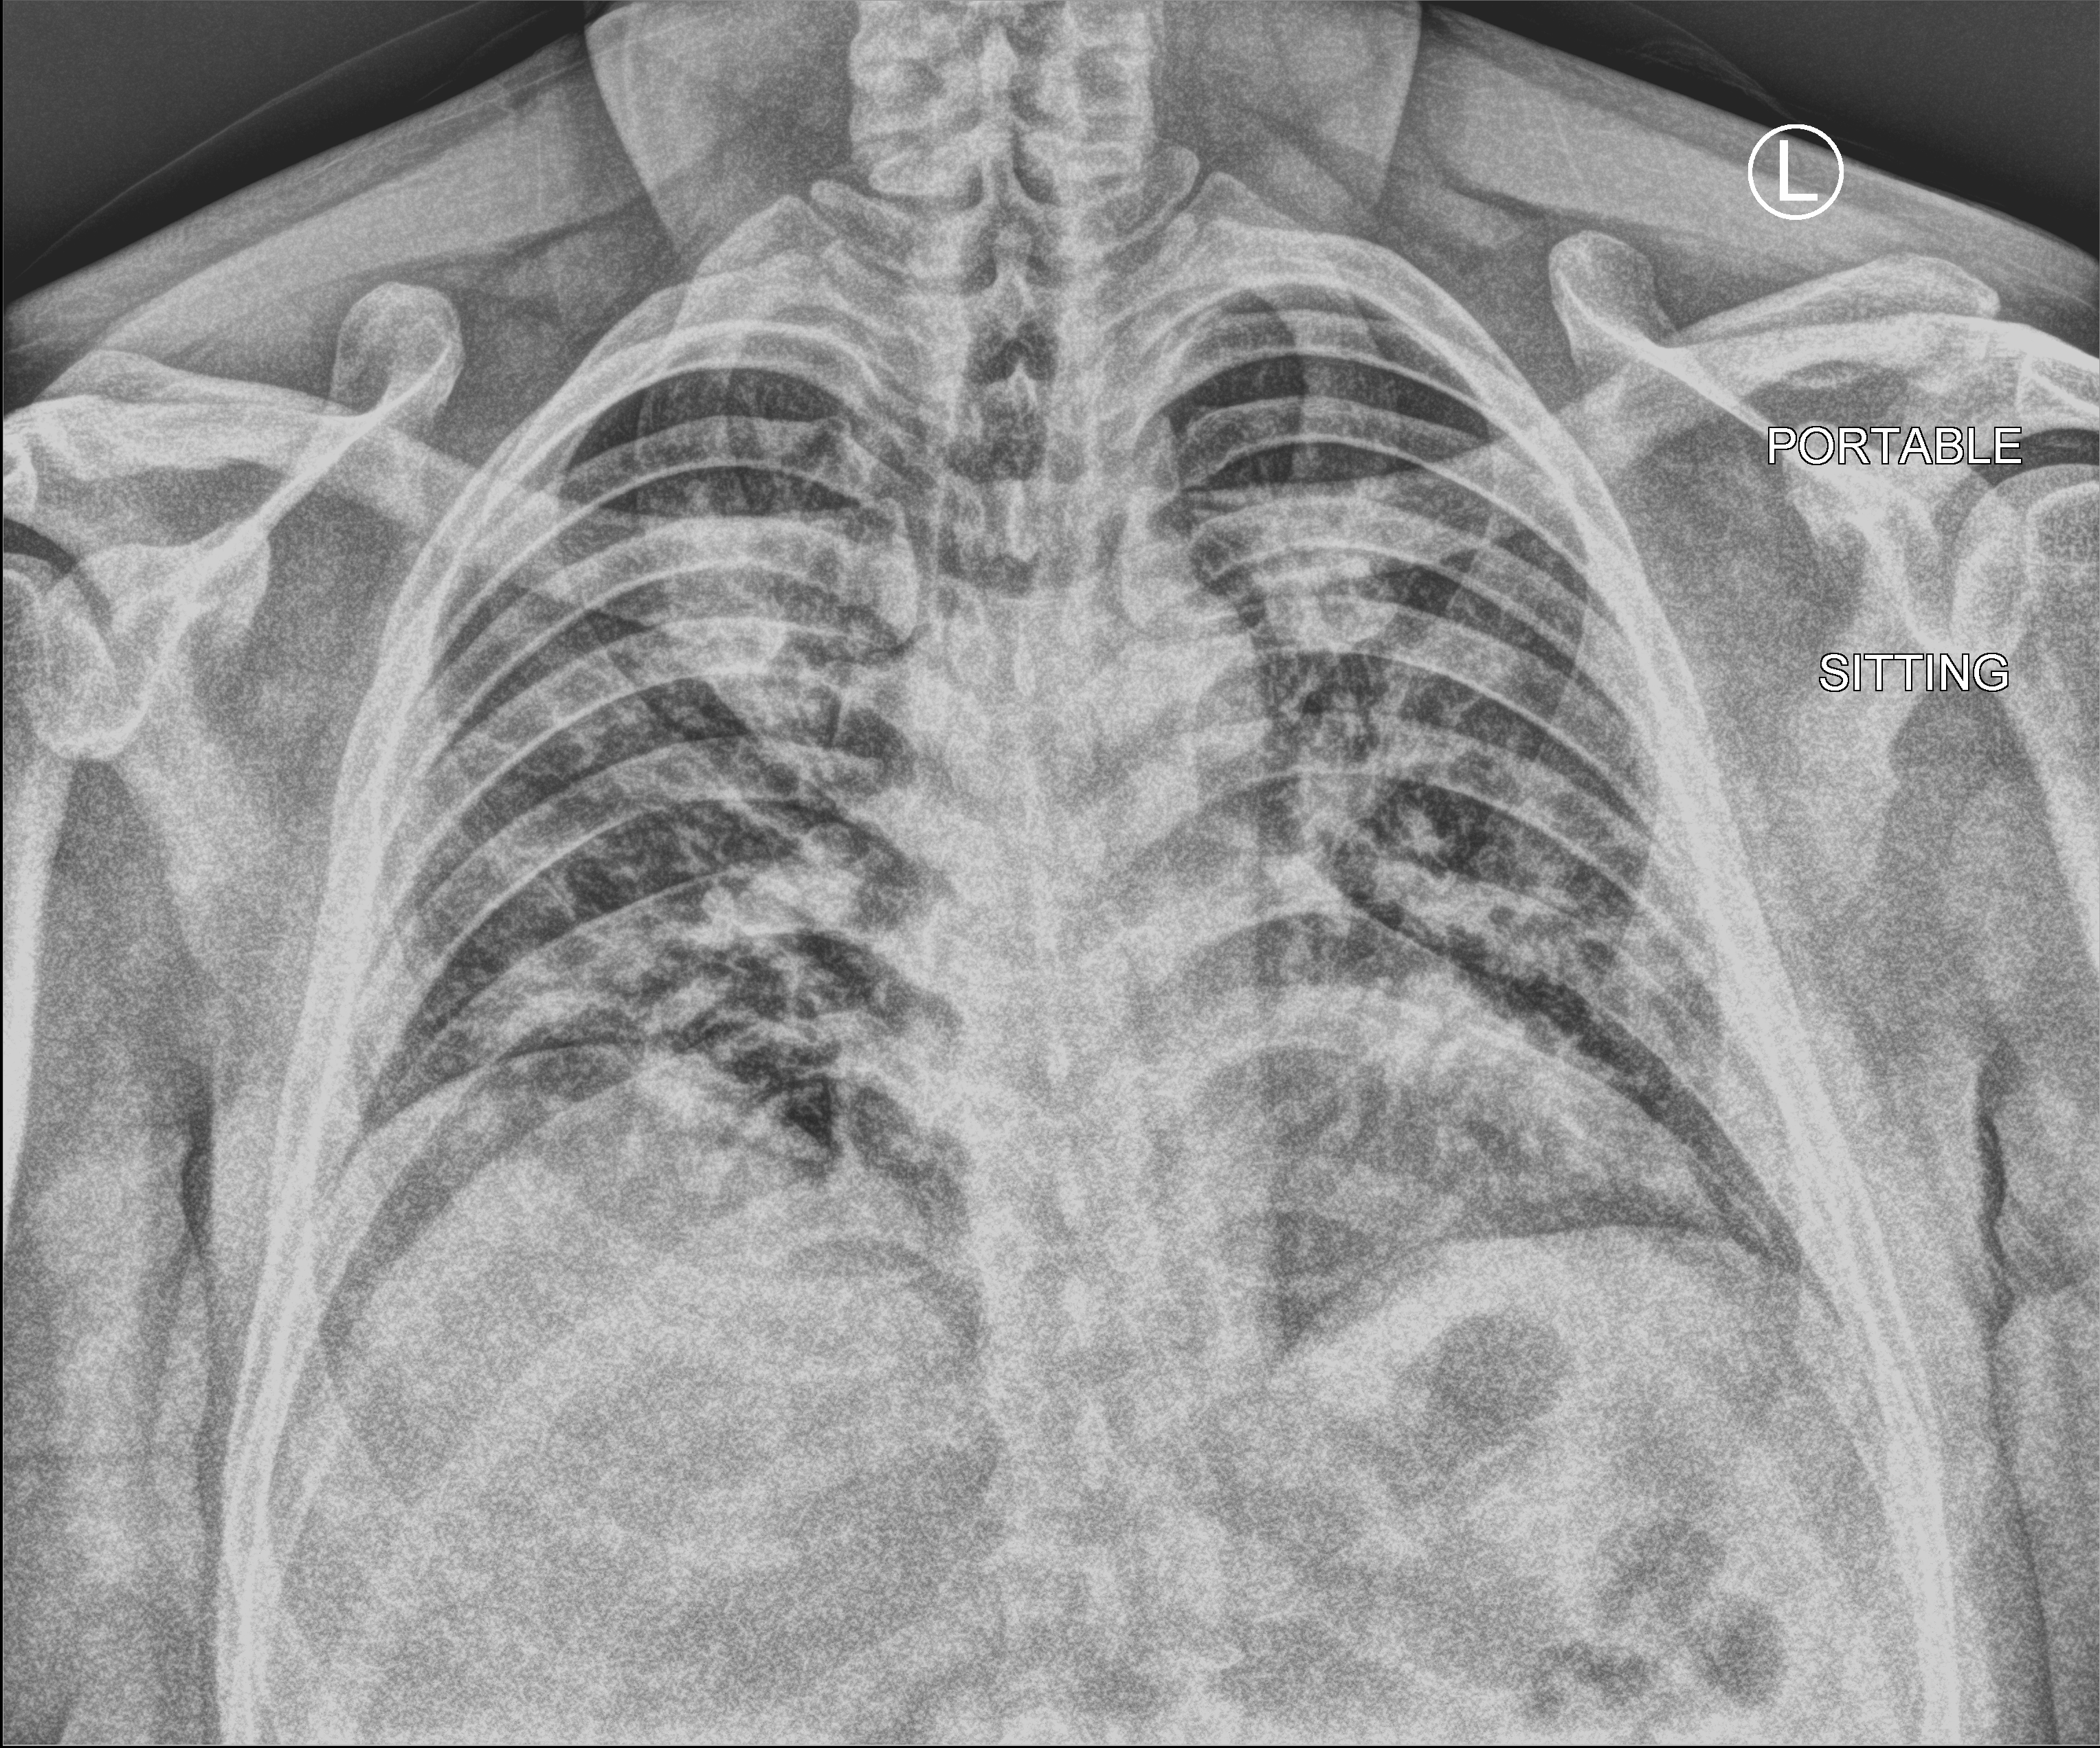
Bedside chest radiograph (computed radiography), anteroposterior (AP) projection. Male patient hospitalised with COVID-19, age 18–59 years.
Hospital-stay facts (about this admission, not read from this image; timing relative to this image not recorded): admitted to intensive care during this hospital stay: yes; mechanically ventilated during this hospital stay: yes.